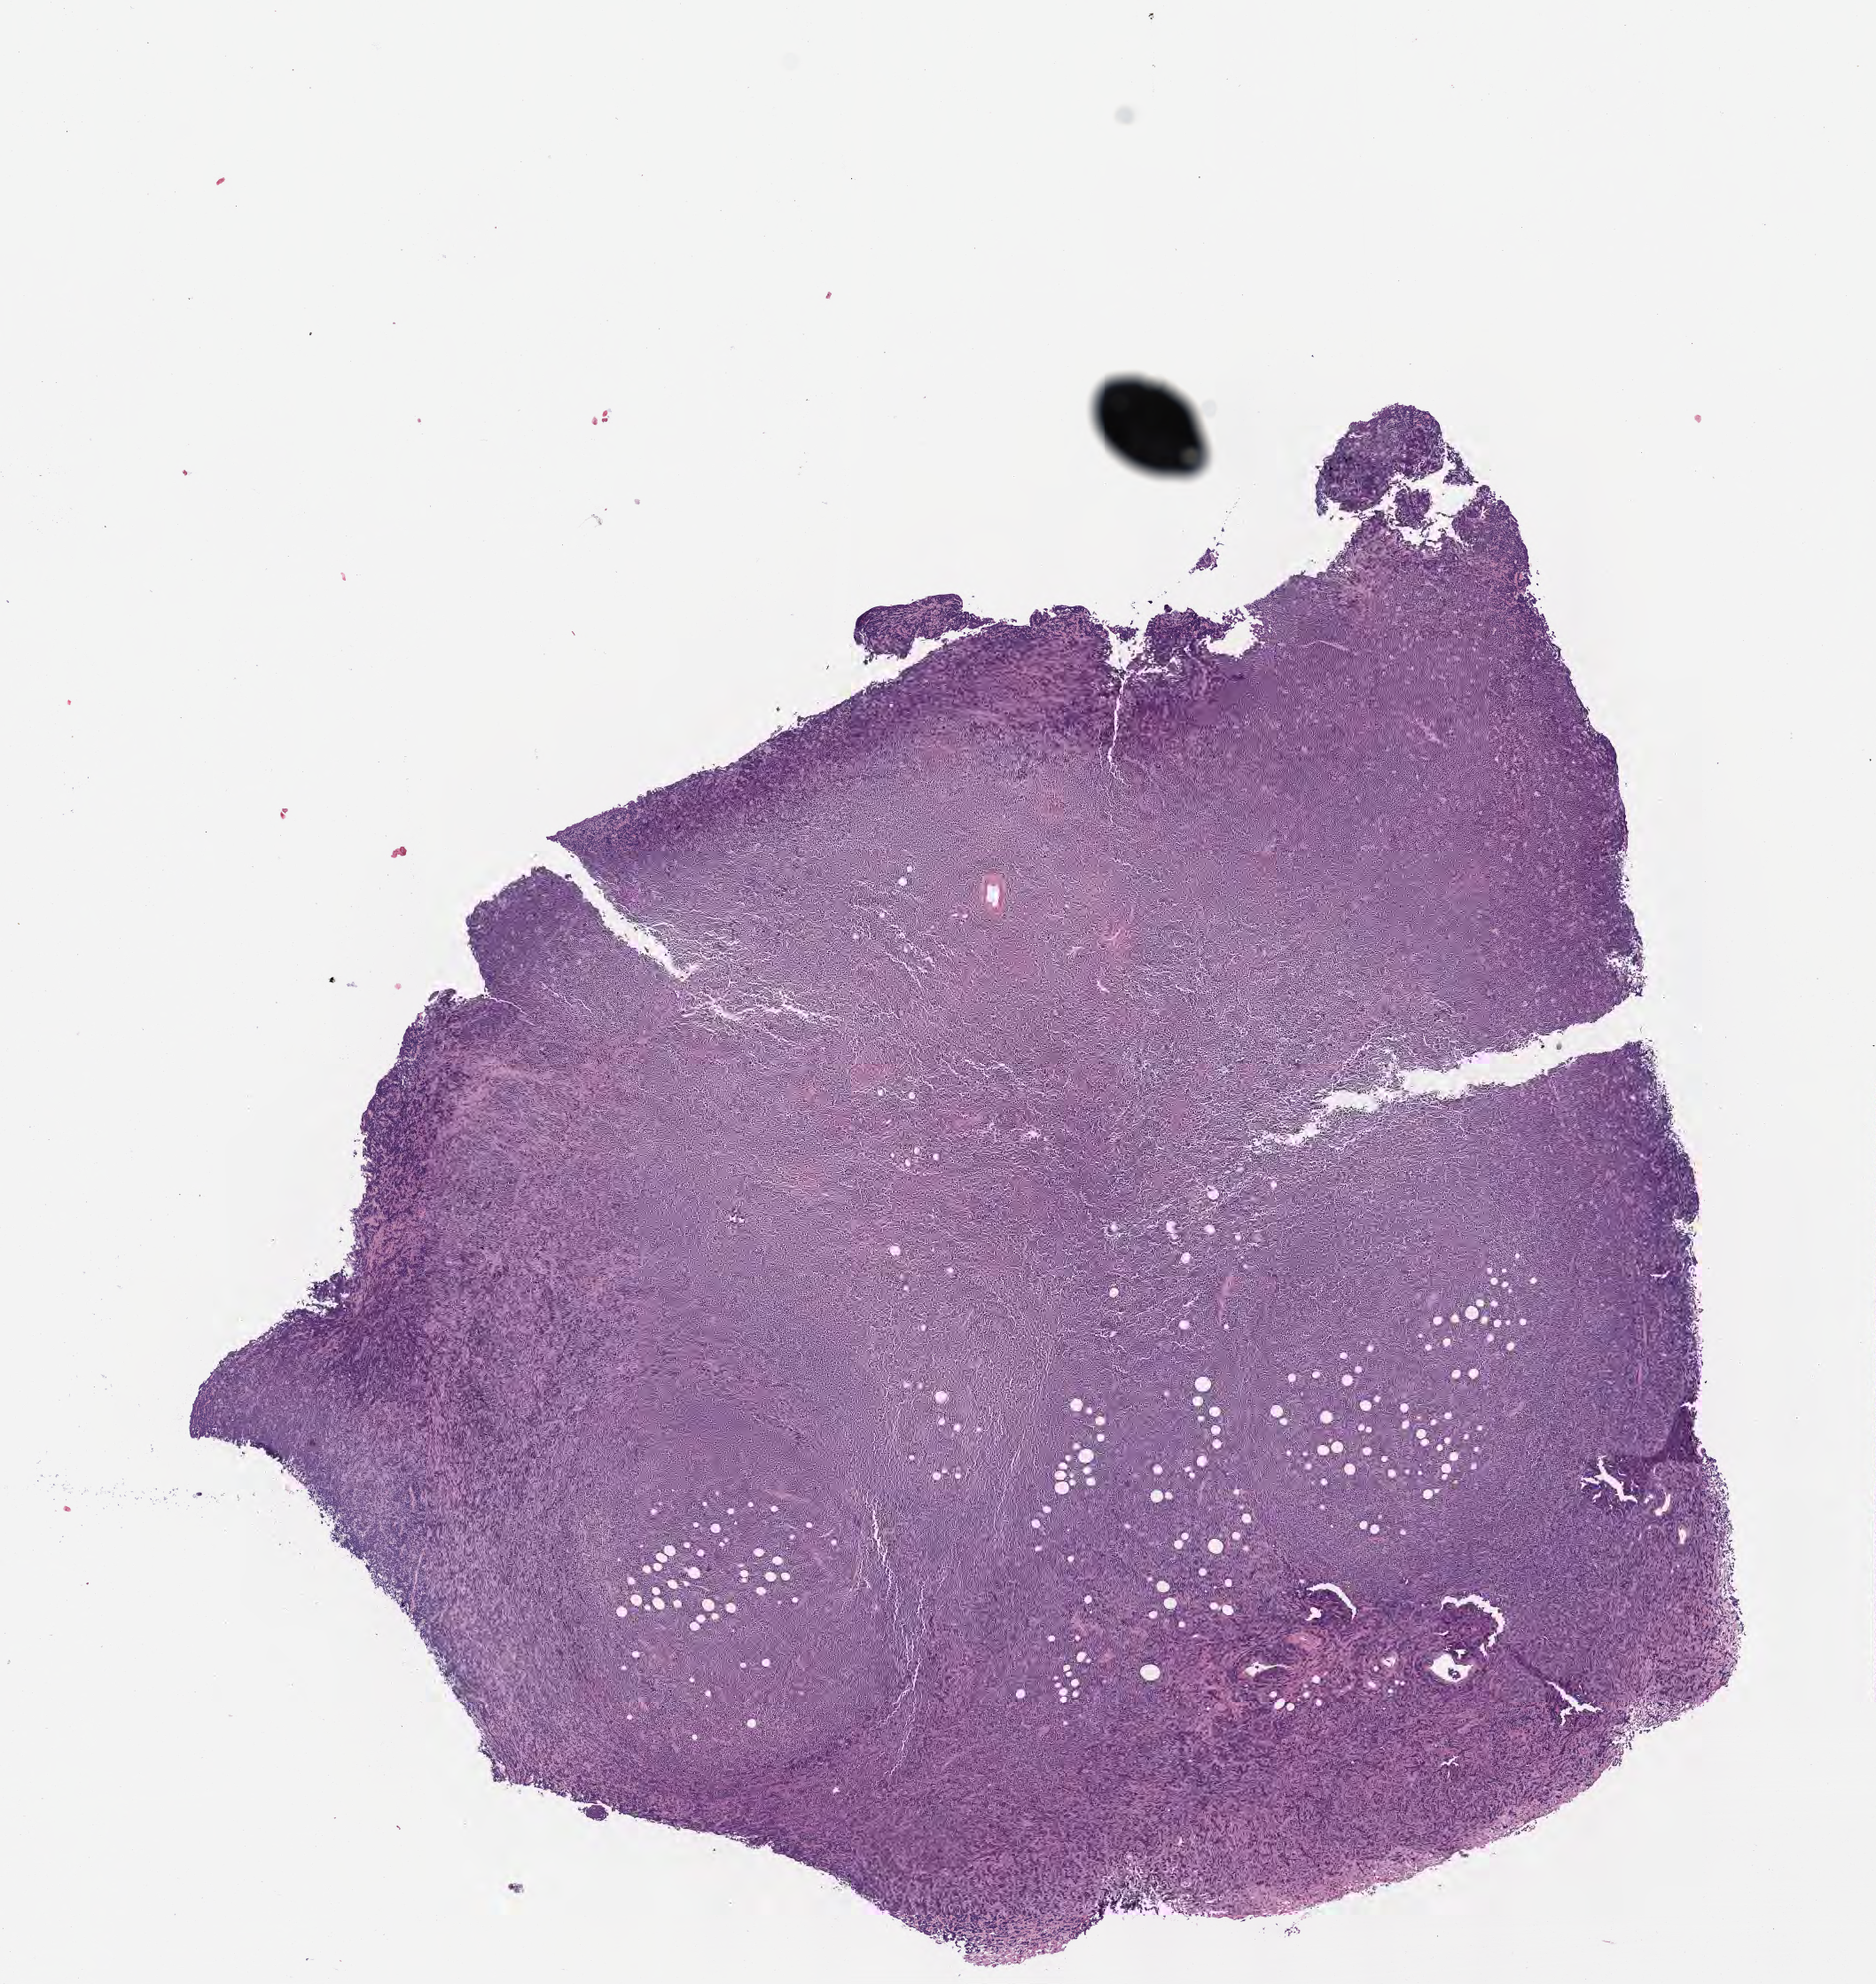
Whole-slide image, H&E stain — whole scanned area (about 8.6 x 9.0 mm) shown as a low-resolution overview; tumor tissue; anatomic site: retroperitoneum. Male, age 7 years at initial diagnosis.
* diagnosis: Diffuse large B-cell lymphoma, NOS